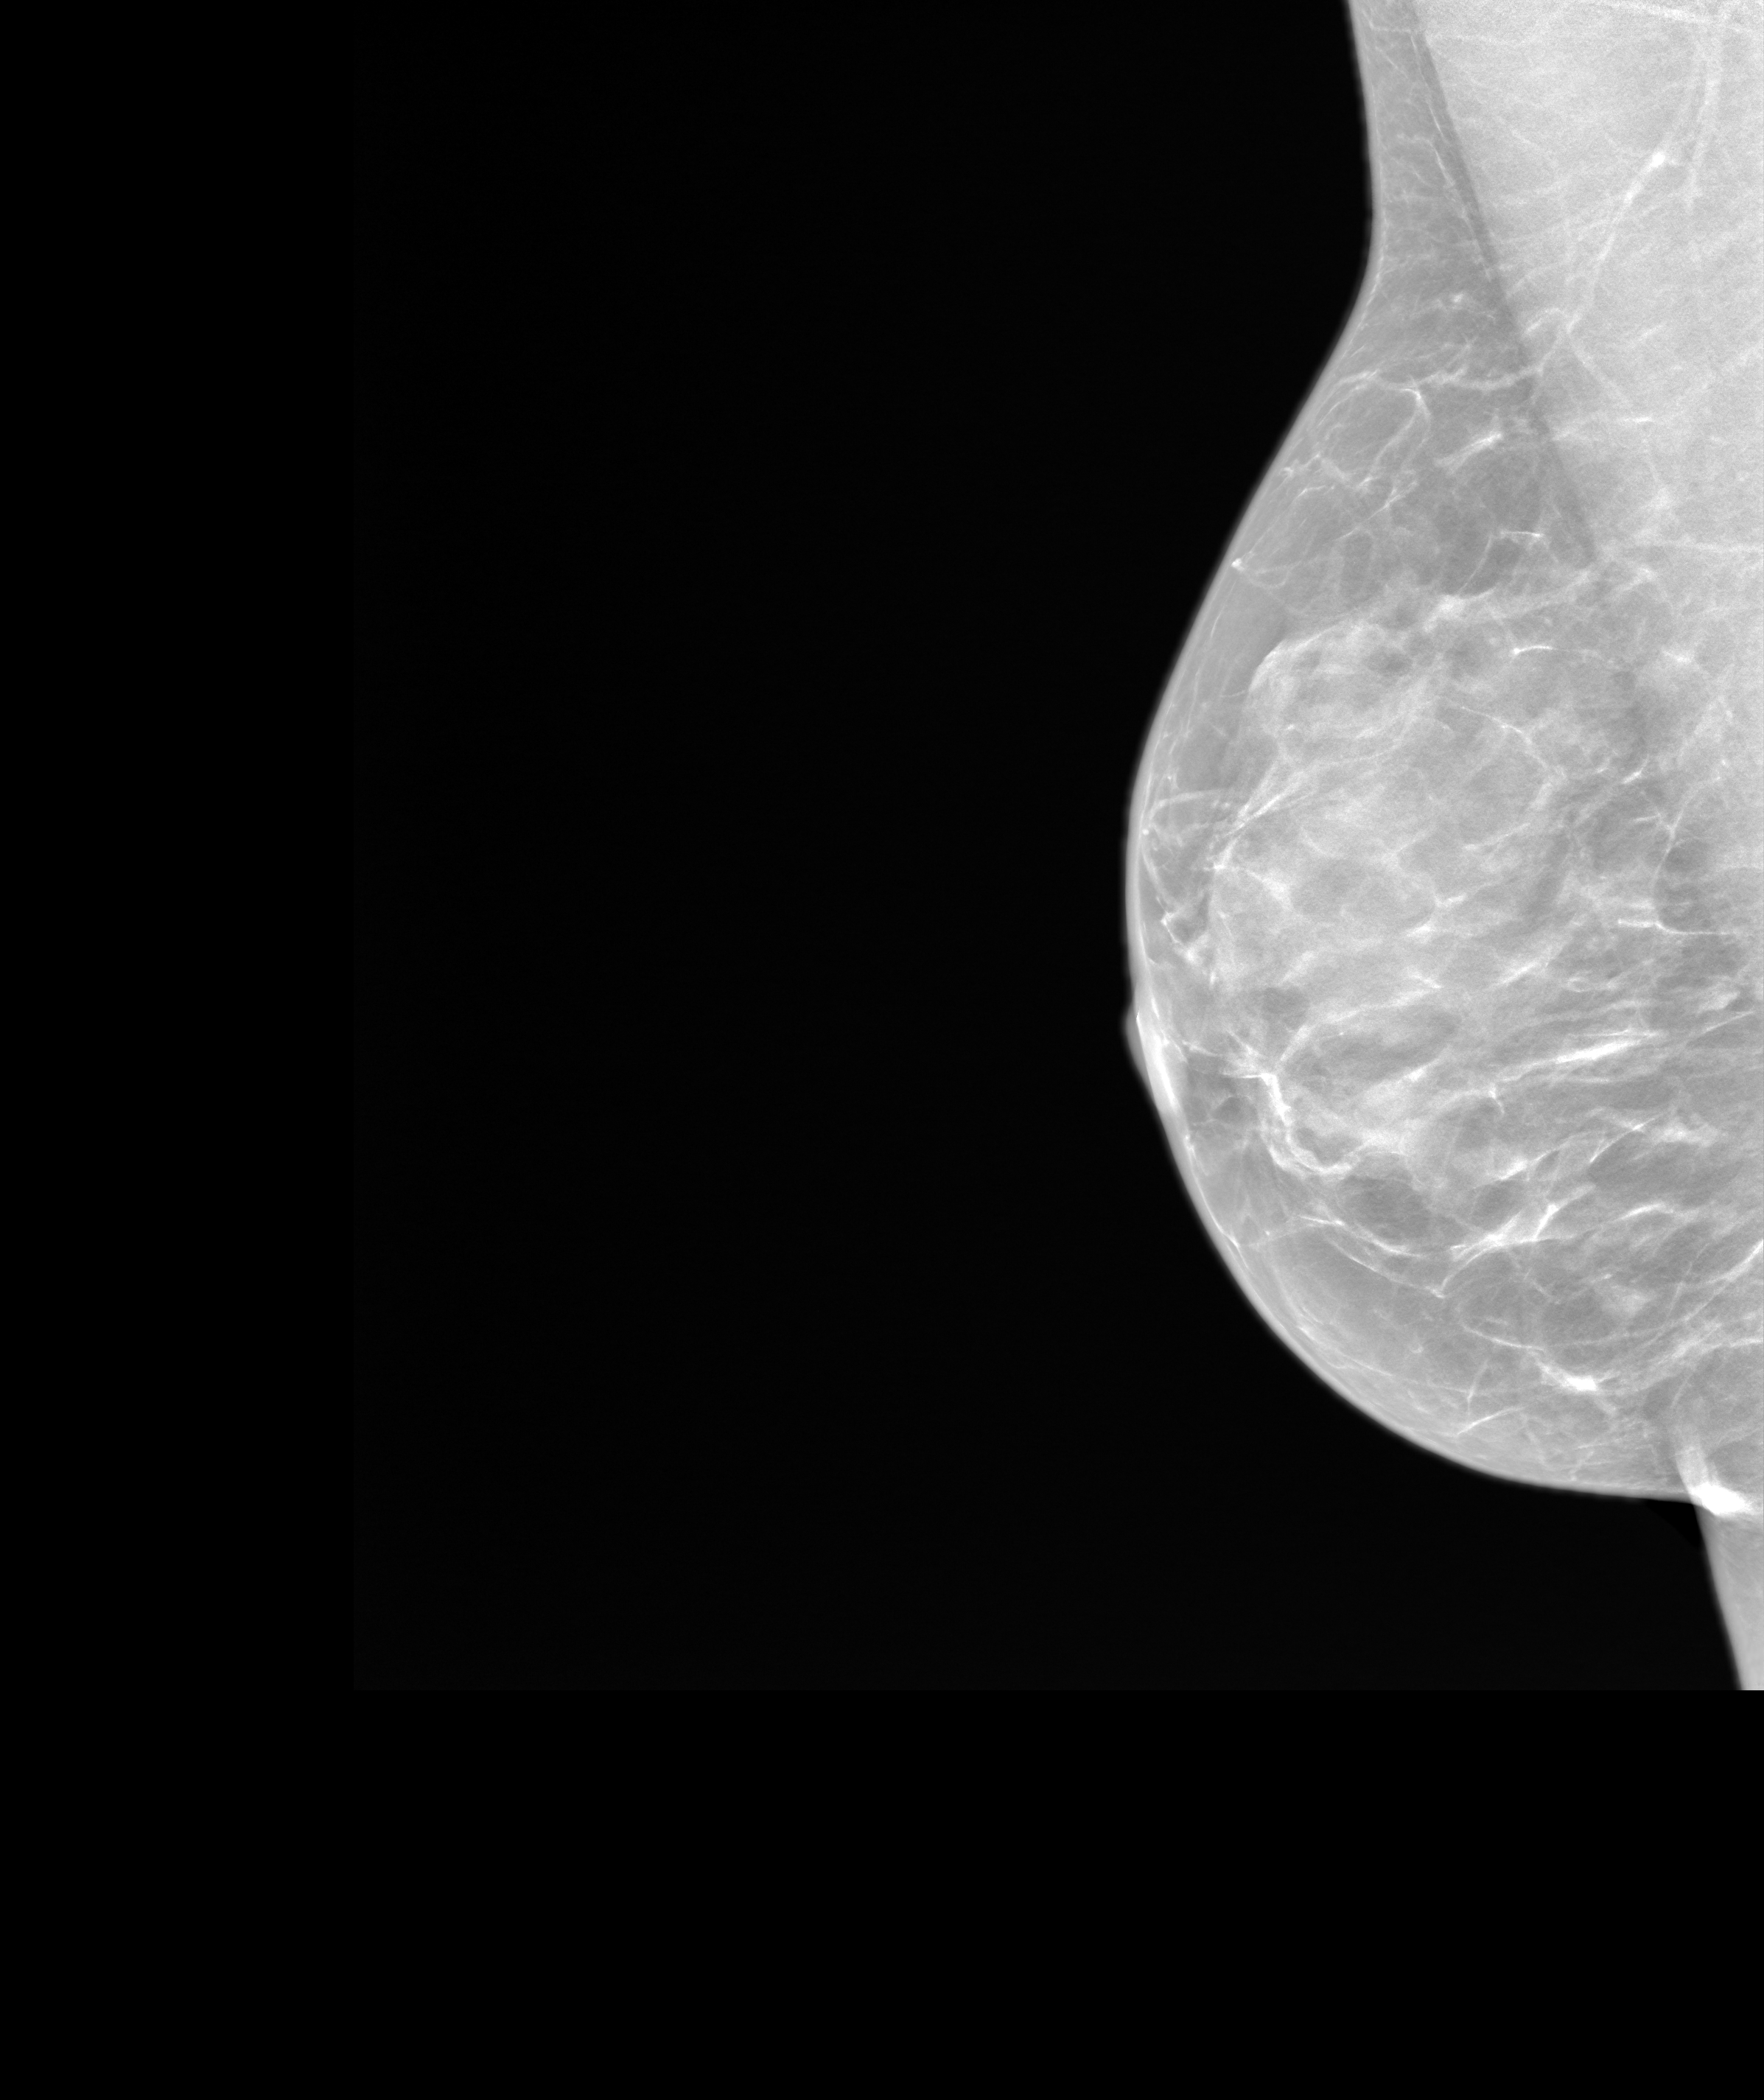
Annual screening mammography examination. Patient: female, 48 years.
Image type: synthesized 2-D view from tomosynthesis. Breast: right. Projection: mediolateral oblique (MLO) view.